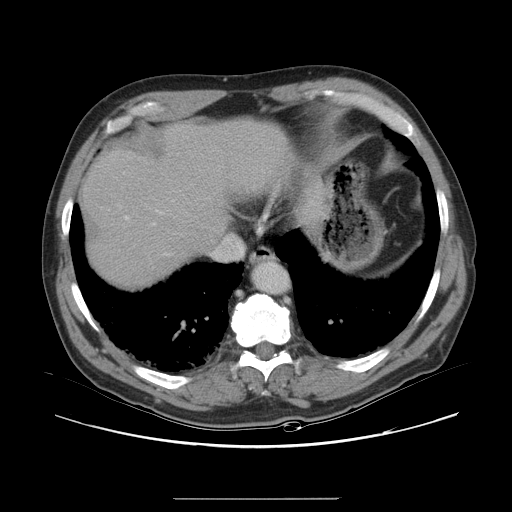
Contrast-enhanced abdominal CT, one axial slice. Slice 28 of 40 in the series (ordered by position). 120 kVp. Intravenous contrast given. Soft-tissue window (W 400 / L 40 HU). 5 mm slice thickness. 512 × 512 image matrix, field of view 408 × 408 mm. Male patient, age 64 years. Case-level facts recorded for this patient, not image findings: diagnosis: colorectal cancer liver metastases, imaged before liver resection; multiple liver metastases: yes; largest metastasis: 3.2 cm; chemotherapy before resection: yes.
Annotated regions visible in this slice (outlined manually by an expert reader):
- hepatic veins: bounding box (x1, y1, x2, y2) in pixels: (166, 254, 170, 255)
- liver: (84, 120, 292, 283)
- planned liver remnant (the part of the liver to remain after resection): (84, 120, 292, 267)
- portal vein (with intrahepatic branches): (126, 217, 128, 219)